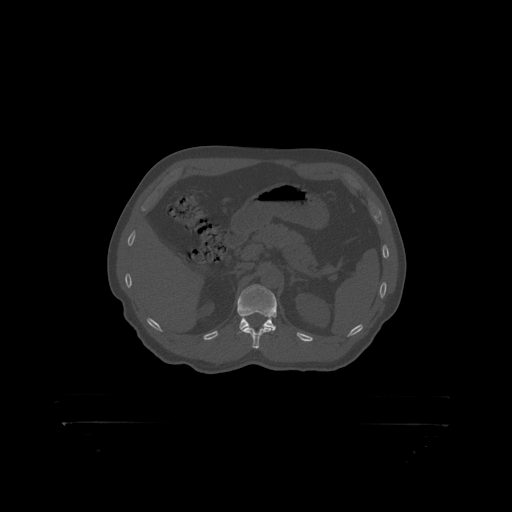
CT including the spine, one axial slice. Reconstruction kernel STANDARD. Bone window (W 1800 / L 400 HU). 1.25 mm slice thickness. 512 × 512 image matrix. Male patient, age 46 years. From the clinical record (not read from this slice): primary cancer: skin.
Annotated regions visible in this slice (semi-automatic segmentation, software-assisted and operator-edited):
- L1 vertebra: box from (x=238, y=285) to (x=277, y=318) px